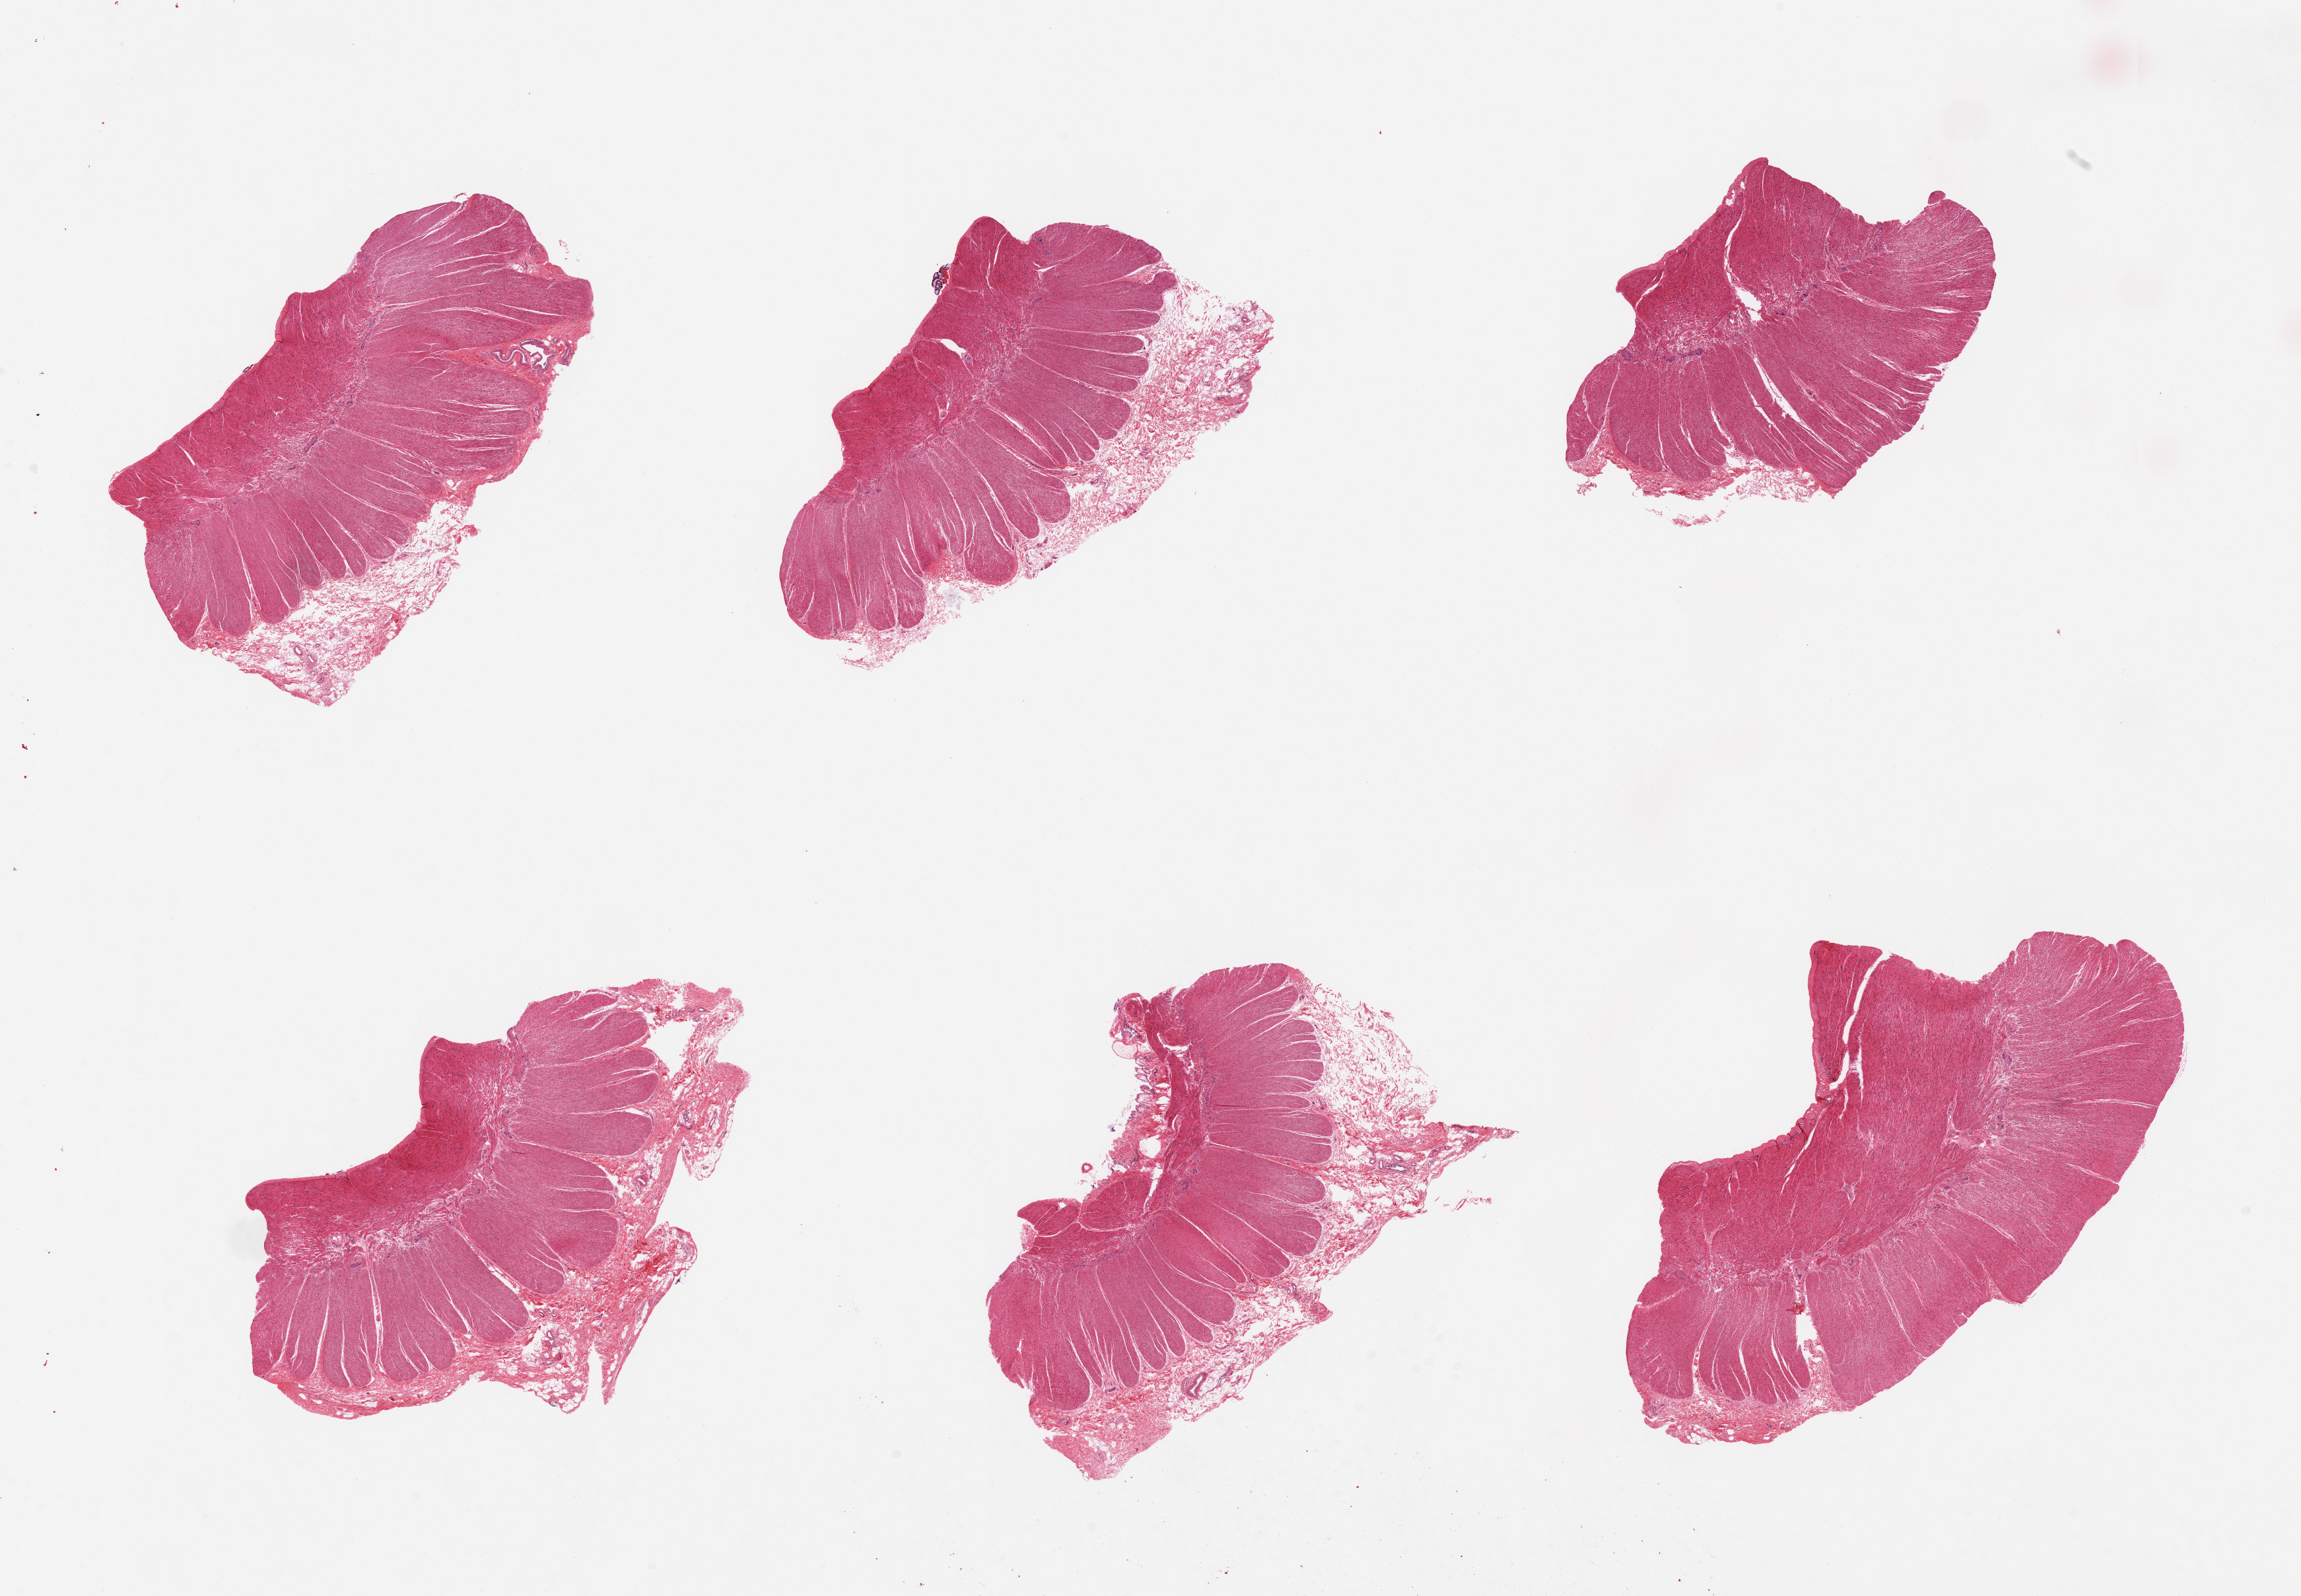
Whole-slide image, hematoxylin and eosin (H&E) stain, brightfield — whole scanned area (about 27.6 x 19.1 mm, acquisition: 20x scan) shown as a low-resolution overview. PAXgene-fixed, paraffin-embedded tissue. Section of sigmoid colon (target tissue). Tissue donor sample. Donor: female.
Reviewer comment on this tissue sample: 6 pieces, good muscularis; focal adherent serosal fat.